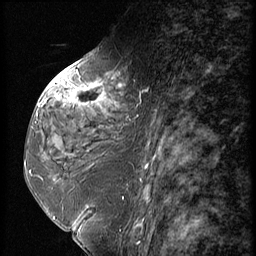
Breast MRI (dynamic contrast-enhanced), one sagittal slice. Dynamic contrast-enhanced series, image 2 of 3 at this slice position (ordered by acquisition). 1.5 T. TE 4.2 ms, TR 9 ms. 2.5 mm slice thickness. 256 × 256 image matrix, field of view 180 × 180 mm. Patient: female, 59 years. Case-level facts recorded for this patient, not image findings: setting: breast cancer imaged before/during neoadjuvant chemotherapy; receptor status: HER2-positive.
Annotated regions visible in this slice (semi-automatic segmentation, software-assisted and operator-edited):
- analysis volume of interest (the breast-tissue region the enhancement analysis was run in; not a lesion): box from (x=44, y=66) to (x=151, y=135) px
- tumour enhancement mask (voxels above the 140 % enhancement threshold inside the analysis volume of interest): (x=51, y=77)–(x=113, y=103)